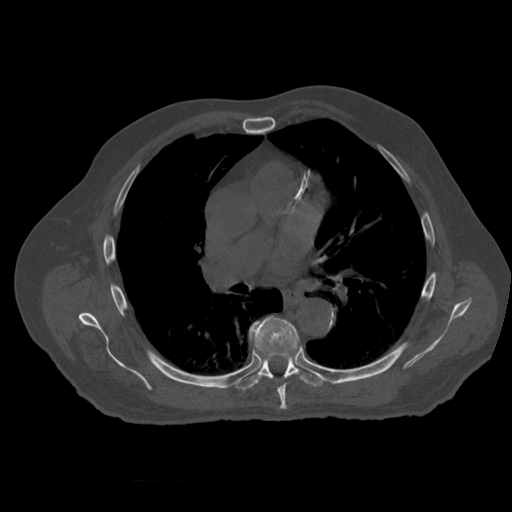
CT including the spine, one axial slice; slice 371 of 399 in the series (ordered by position); bone window (W 1800 / L 400 HU); 1.25 mm slice thickness; 512 × 512 image matrix, field of view 407 × 407 mm. Patient age 73 years. From the clinical record (not read from this slice): primary cancer: prostate; vertebrae with lytic lesions (as recorded): L2.
Structures marked on this image (semi-automatic segmentation, software-assisted and operator-edited):
- T6 vertebra: bounding box [x1, y1, x2, y2] px = [250, 316, 299, 411]
- T7 vertebra: [235, 323, 328, 391]